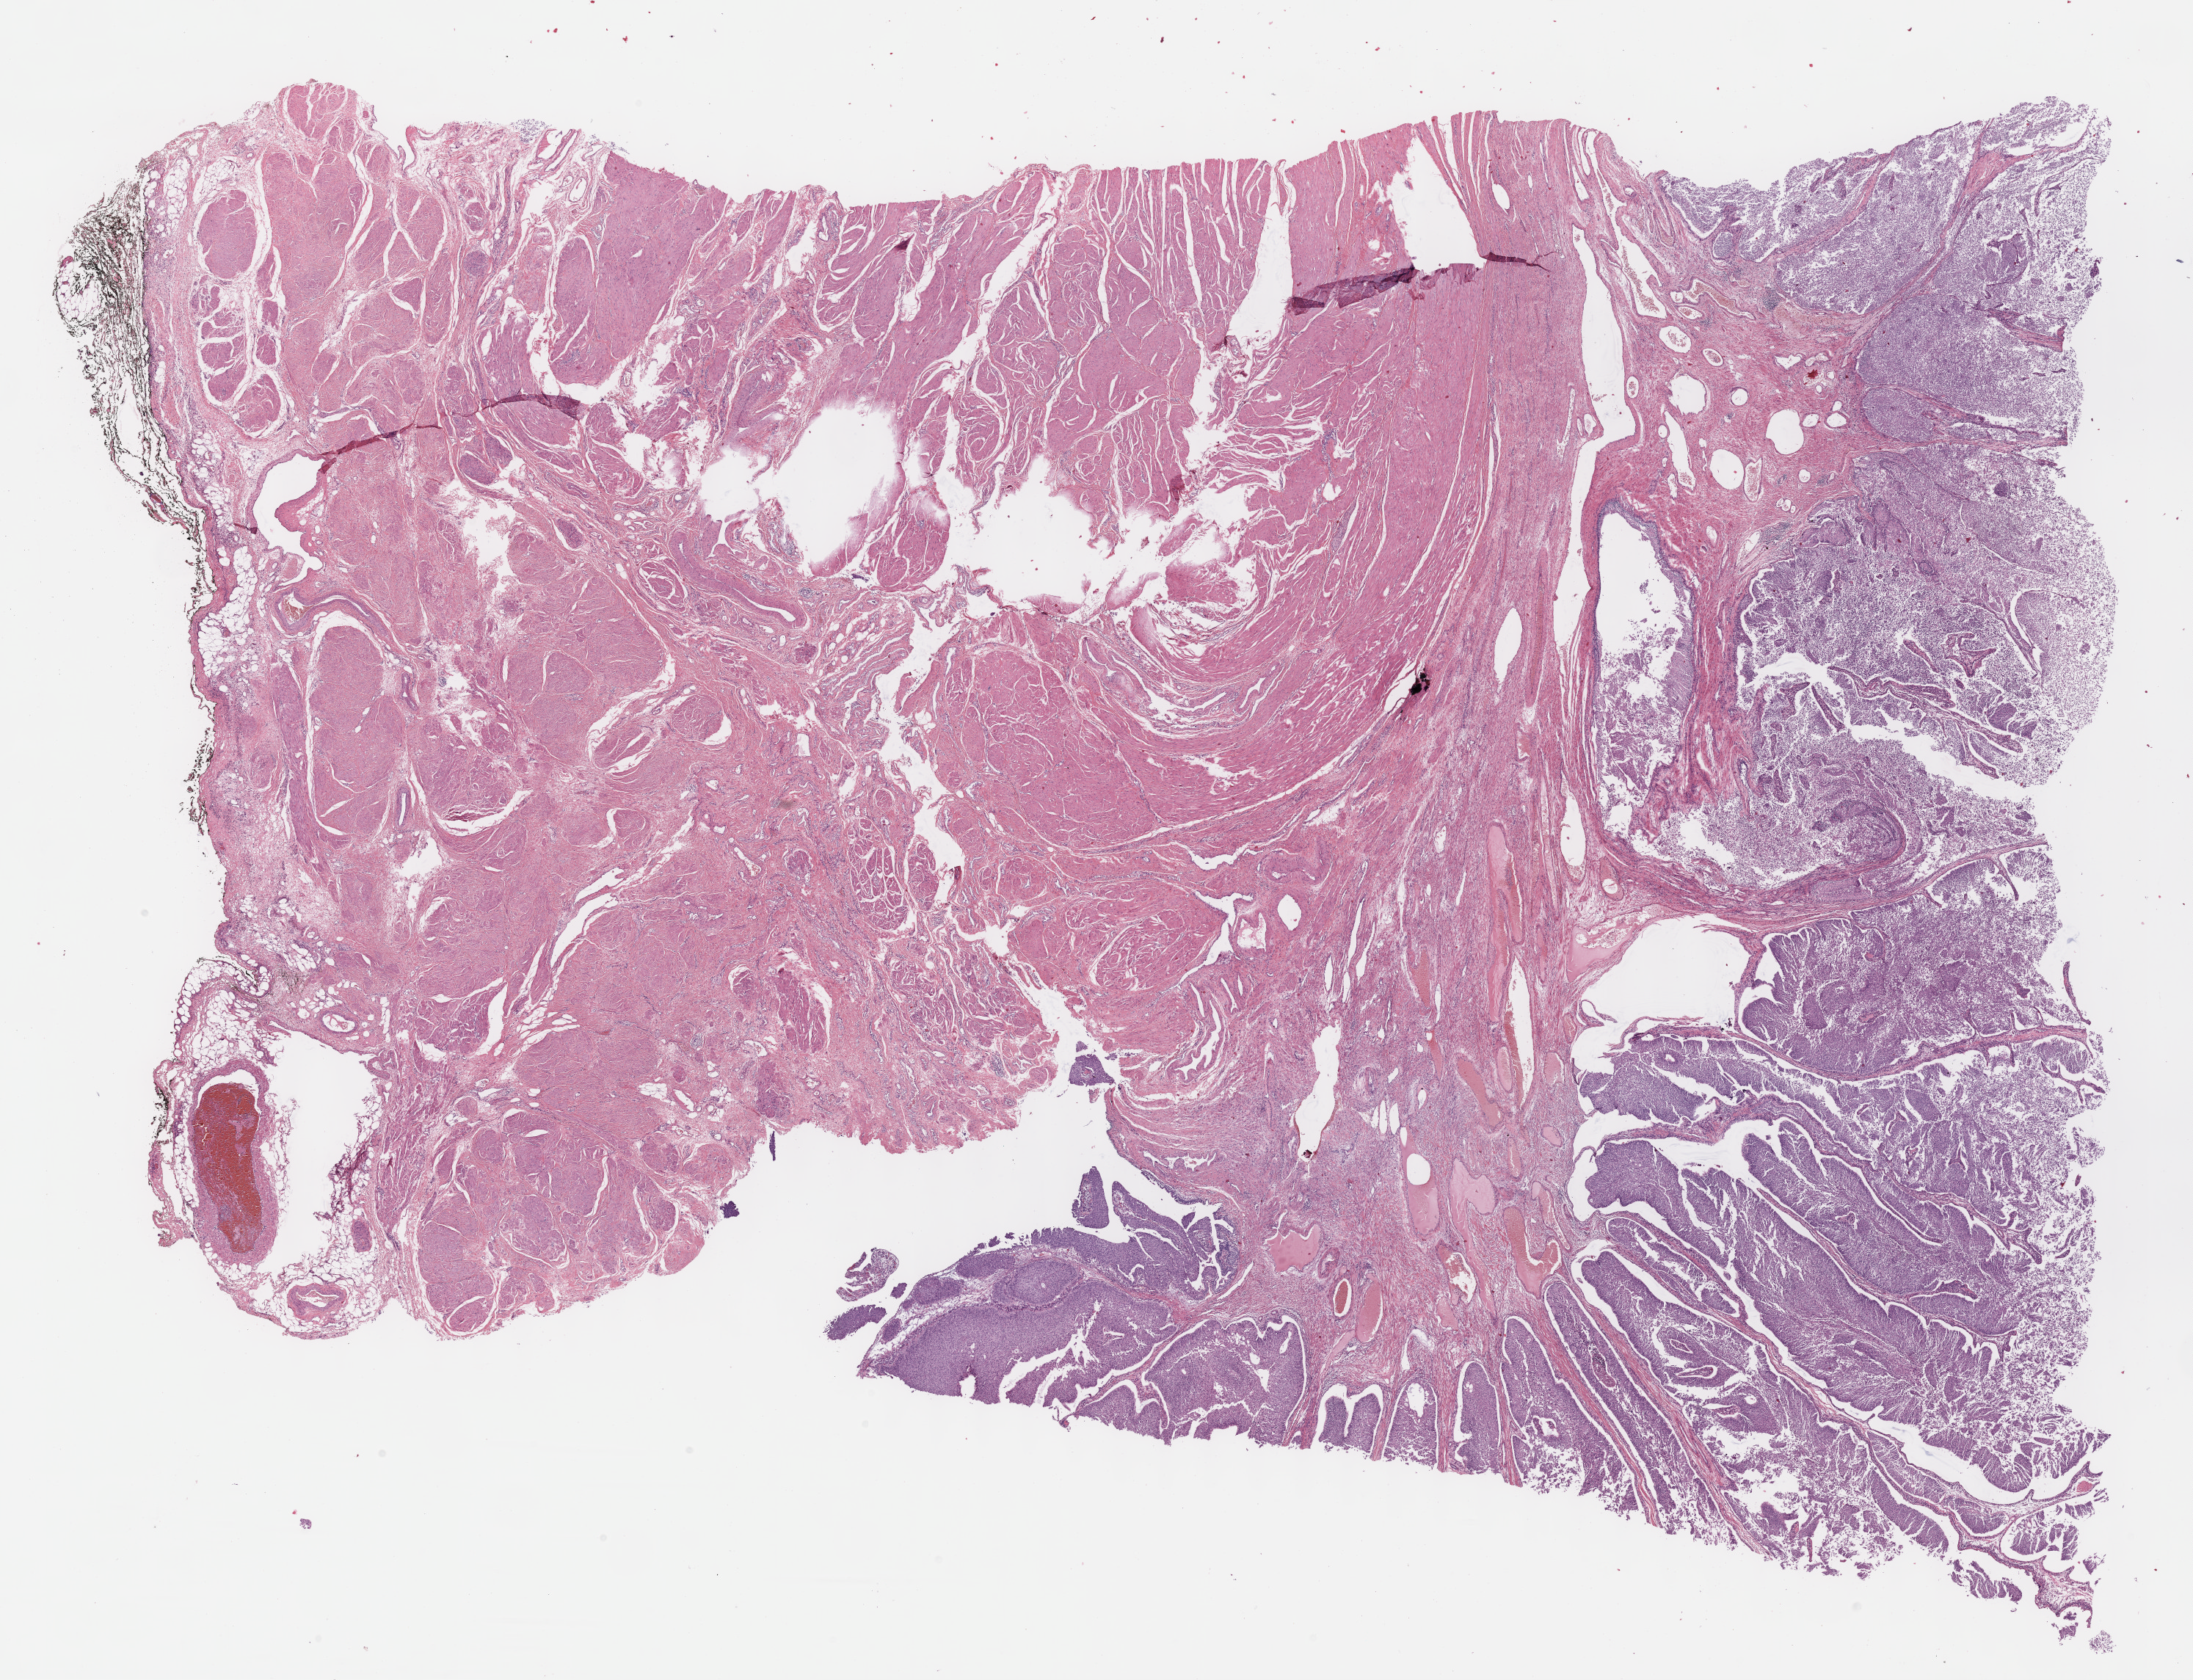
Digitized Hematoxylin and eosin (H&E) stained tissue section (whole slide) — whole scanned area (about 24.1 x 18.5 mm, from a 40x scan) shown as a low-resolution overview. FFPE section. Bladder, primary tumour sample. Patient: male, age at initial diagnosis 52 years. Histologic grade: high grade.
• AJCC pathologic stage: II (7th edition)
• histologic diagnosis: Papillary transitional cell carcinoma